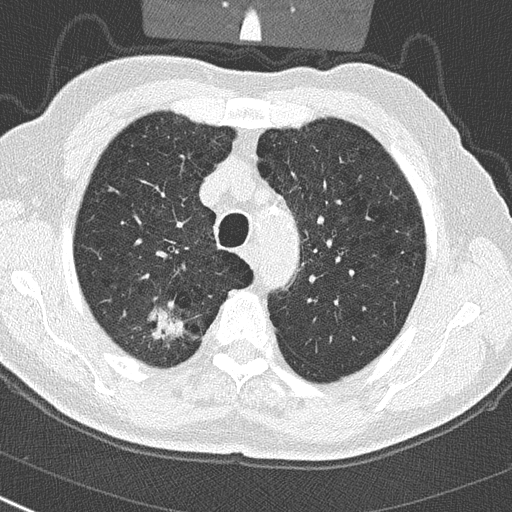
Low-dose screening chest CT, axial slice. Baseline screening round. Lung window (W 1500 / L -600 HU). Lung (sharp) reconstruction kernel (B50f). Slice 68 of 290 in the series. 512 × 512 image matrix. Male participant, aged 65 years at enrolment. Current smoker at enrolment.
Expert-annotated lung lesion, bounding box <131,299,197,358> (left, top, right, bottom; pixels). The exam's reader record, not a measurement of the box and not confirmed to be the same lesion: non-calcified nodule or mass ≥4 mm, right upper lobe, 24 × 19 mm, spiculated (stellate) margins, soft tissue attenuation.